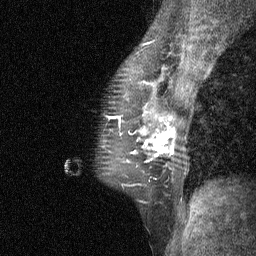
Breast MRI (dynamic contrast-enhanced), one sagittal slice; position 42 of 64 along the scan axis; dynamic contrast-enhanced study with each time point stored as its own series, time point 3 of 4 at this slice position (ordered by acquisition time); 1.5 T; TE 4.8 ms, TR 27 ms; 2 mm slice thickness; 256 × 256 image matrix, field of view 180 × 180 mm. Female patient, age 44 years. From the clinical record (not read from this slice): setting: breast cancer imaged before/during neoadjuvant chemotherapy; receptor status: HR-positive, HER2-negative.
Outlined on this slice (semi-automatic segmentation, software-assisted and operator-edited):
- analysis volume of interest (the breast-tissue region the enhancement analysis was run in; not a lesion): bounding box (x1, y1, x2, y2) in pixels: (115, 117, 185, 188)
- tumour enhancement mask (voxels above the 90 % enhancement threshold inside the analysis volume of interest): (119, 118, 175, 157)